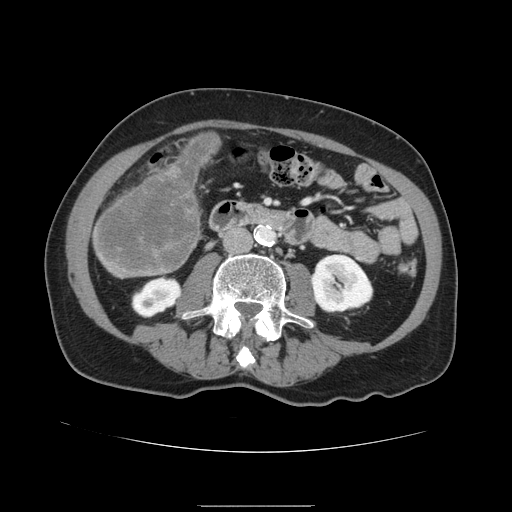
Contrast-enhanced abdominal CT, one axial slice. Slice 32 of 168 in the series (ordered by position). 120 kVp. Intravenous contrast given. Soft-tissue window (W 400 / L 40 HU). 512 × 512 image matrix, field of view 386 × 386 mm. Male patient, age 74 years. From the clinical record (not read from this slice): diagnosis: colorectal cancer liver metastases, imaged before liver resection.
Outlined on this slice (expert manual segmentation):
- liver: bounding box <92,133,221,278> (left, top, right, bottom; pixels)
- liver metastasis: <97,137,217,274>